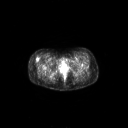
FDG PET of an extremity soft-tissue mass (from a PET/CT study), one axial slice; slice 50 of 267 in the series (ordered by position); 3.27 mm slice thickness; 128 × 128 image matrix, field of view 700 × 700 mm. Female patient, age 34 years. Case-level facts recorded for this patient, not image findings: histological type: synovial sarcoma; grade: intermediate; site of the primary tumour: right thigh.
Outlined on this slice (expert contour drawn on MRI and transferred to this co-registered scan by the dataset authors):
- gross tumour volume including surrounding oedema: bounding box [x1, y1, x2, y2] px = [35, 58, 38, 62]
- gross tumour volume (mass): [35, 58, 38, 62]